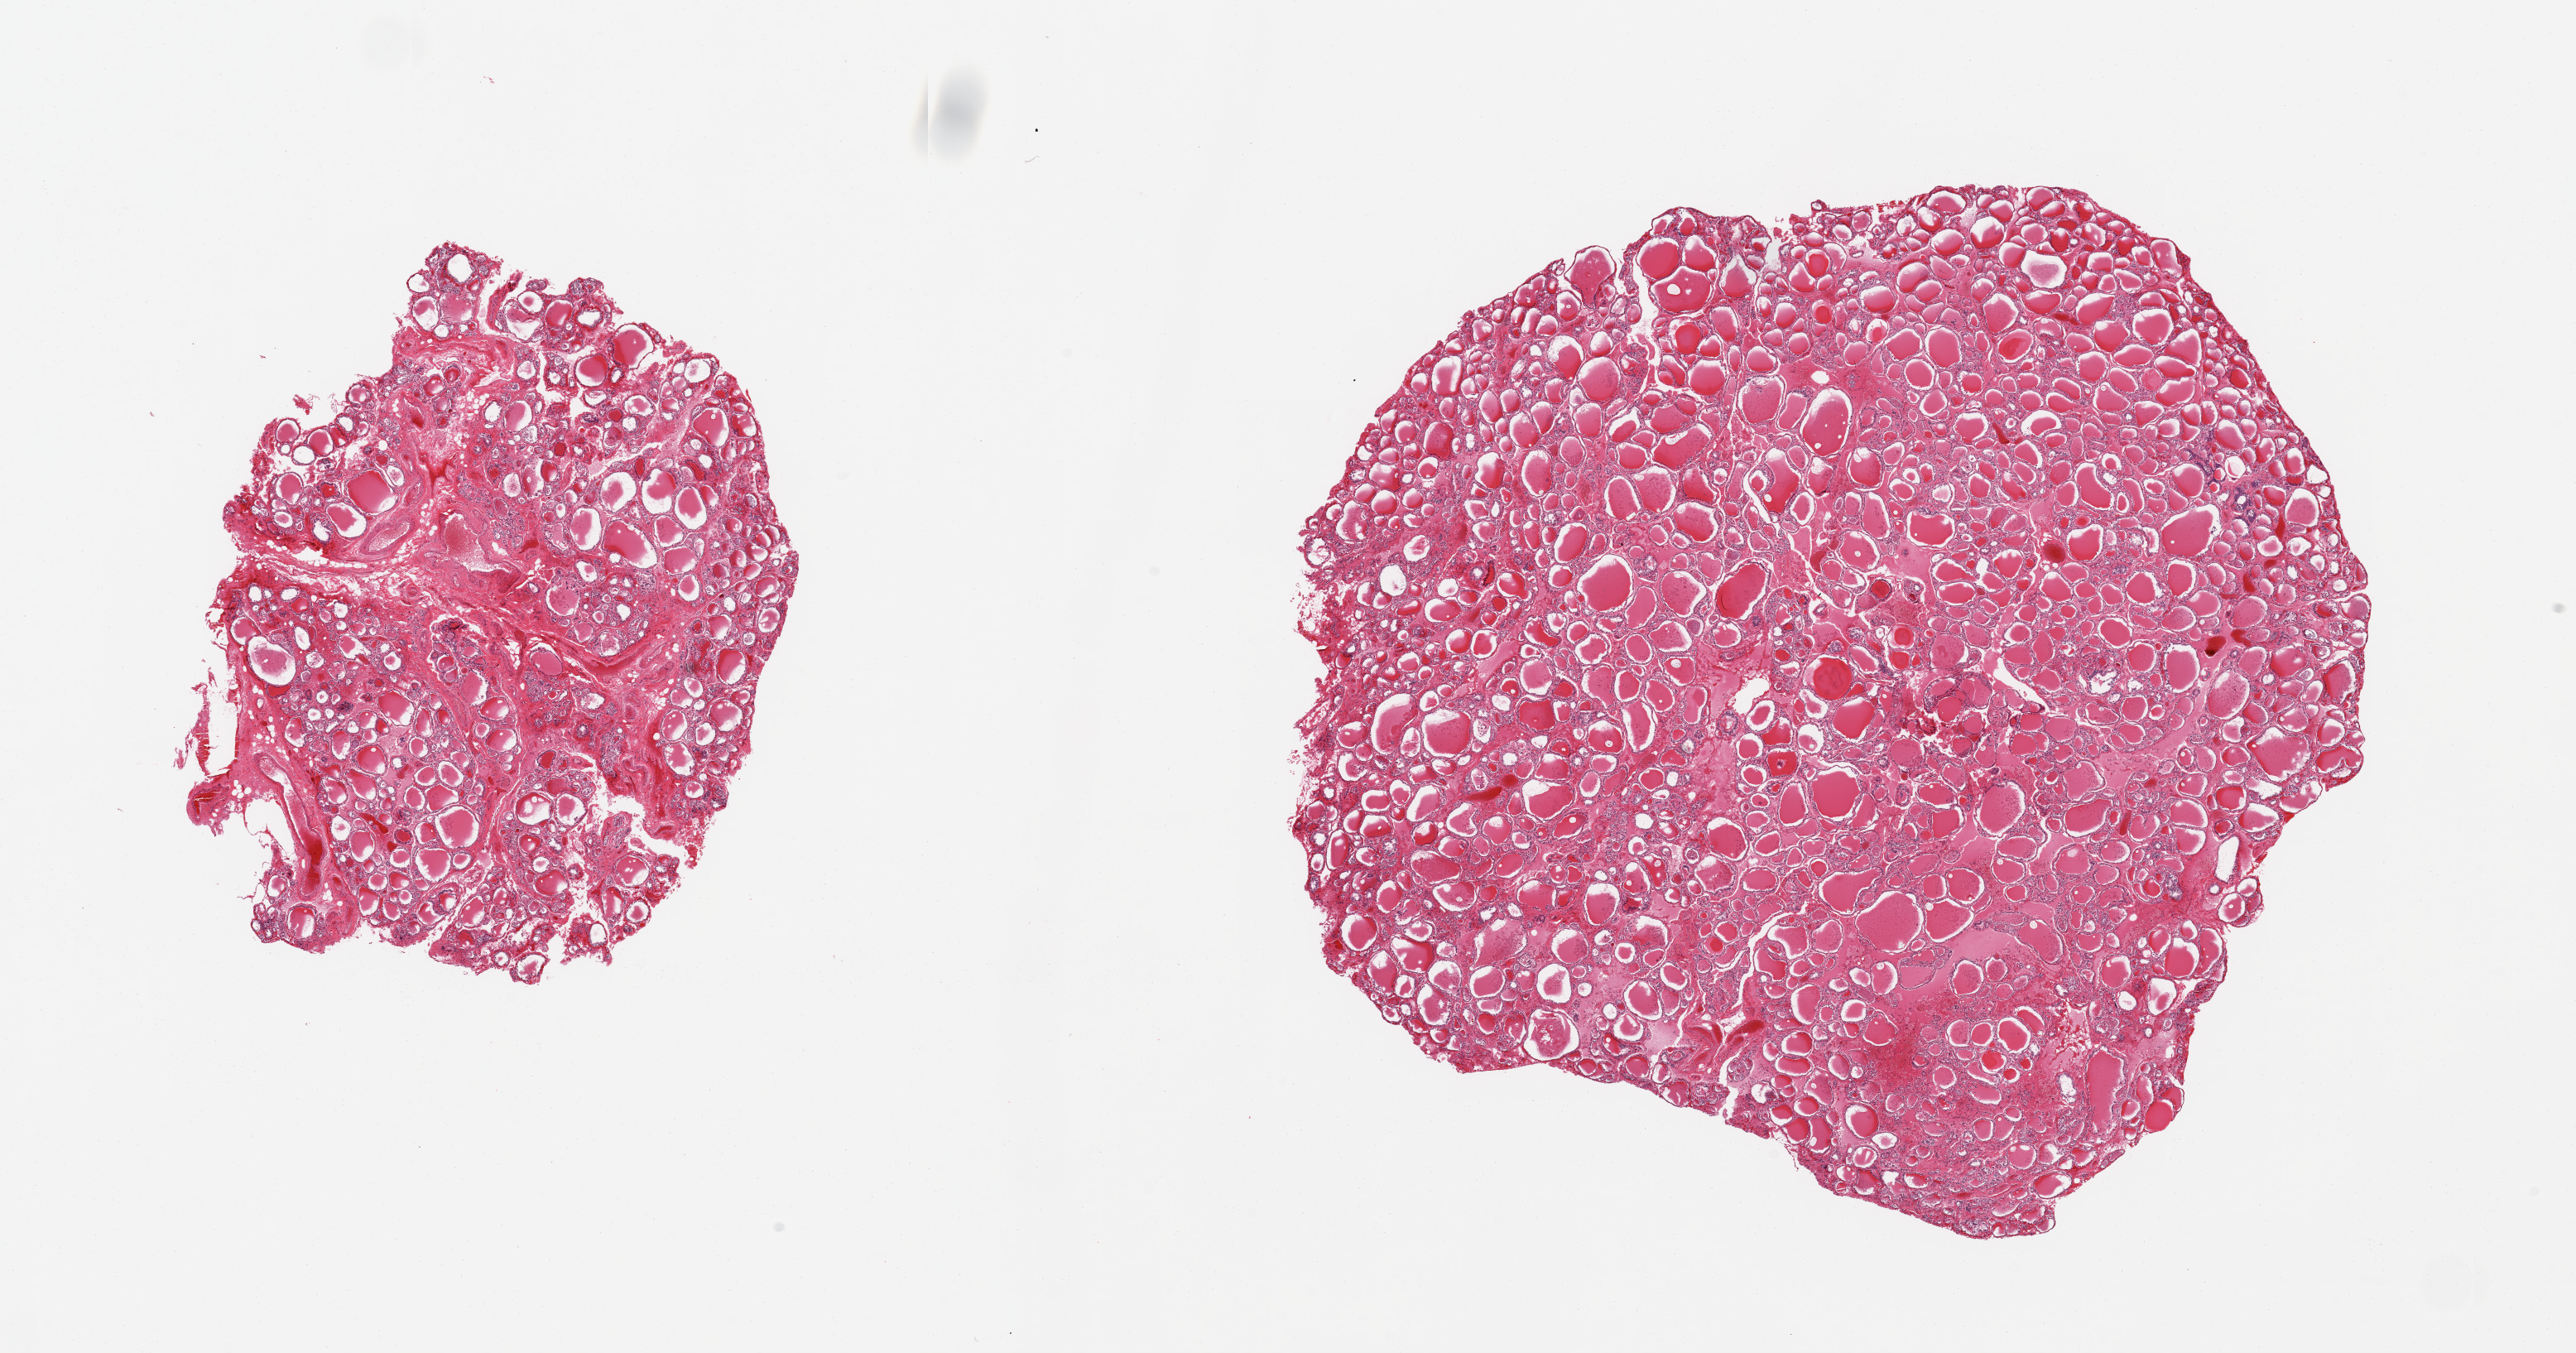
Whole-slide image, H&E stain — shown as a low-resolution overview of the whole scanned area (about 24.6 x 12.9 mm); PAXgene-fixed, paraffin-embedded tissue; target tissue: thyroid; donor tissue sample. Male donor.
Pathologist's review note for this sample: 2 pieces; nodular goiter with regressive changes.